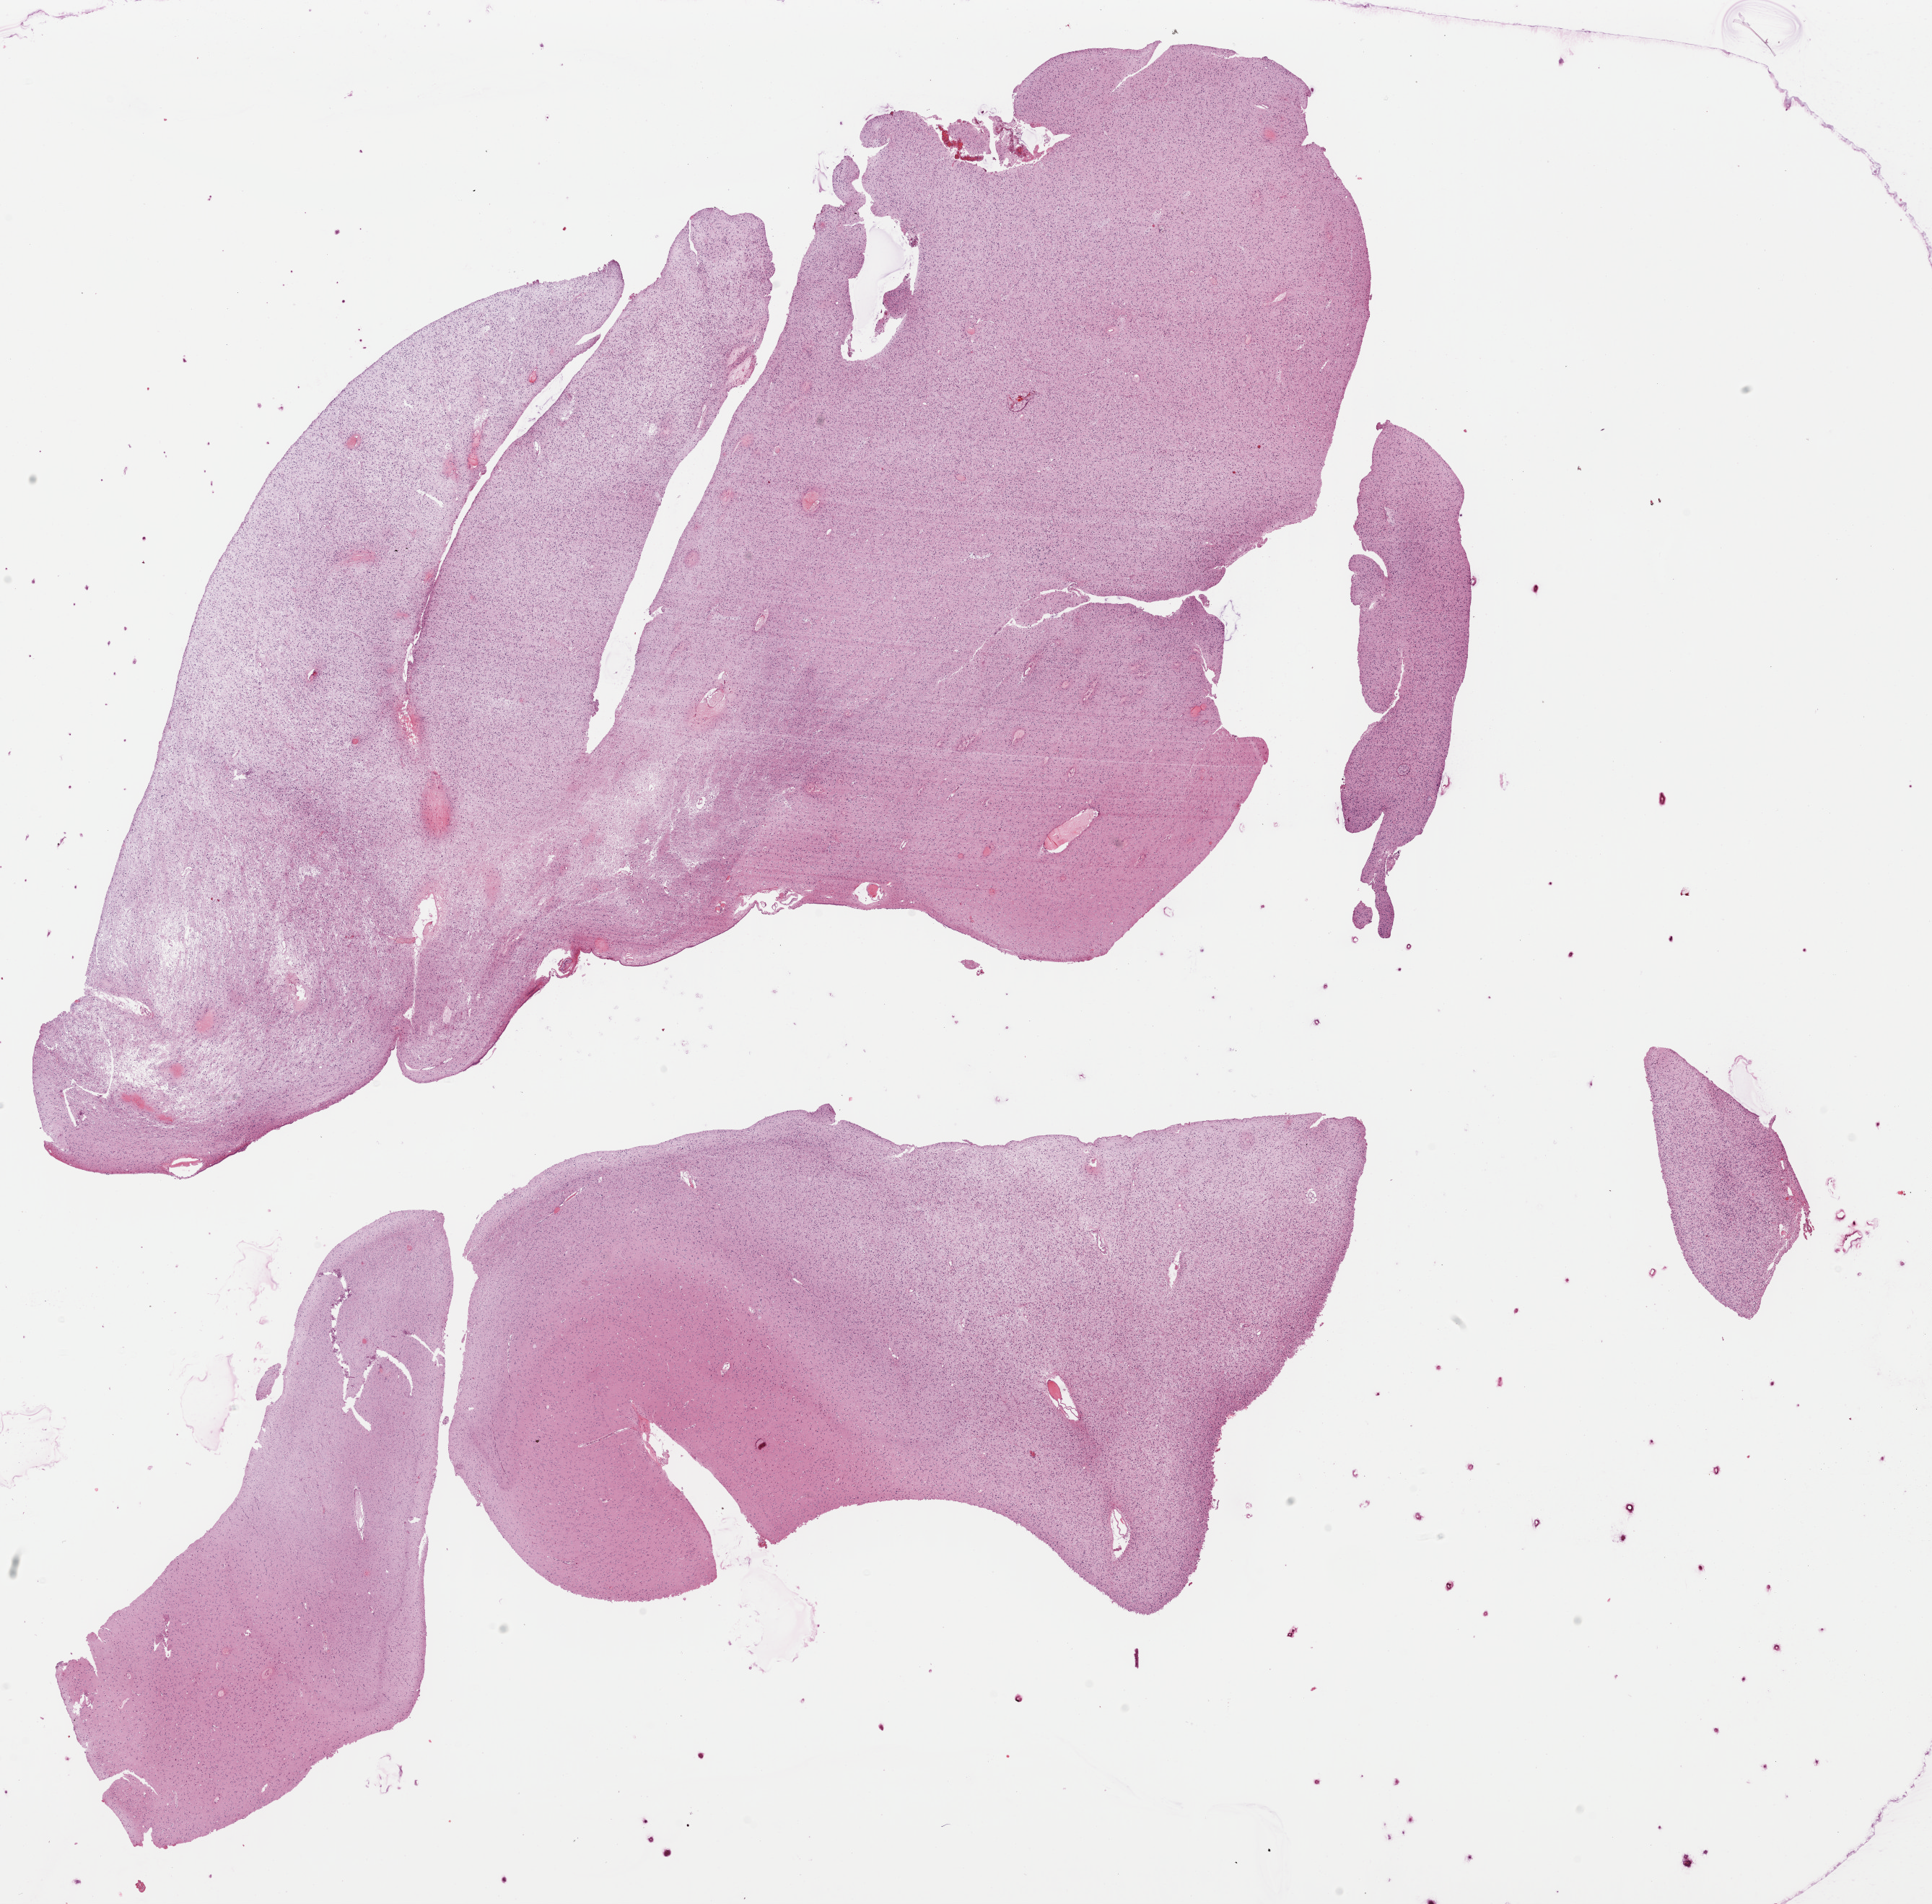
H&E whole-slide image, shown as a low-resolution overview of the whole scanned area (about 21.1 x 20.8 mm), FFPE section, sample: primary tumour, brain. Patient: male, age at initial diagnosis 43 years. Histologic grade: G3 (poorly differentiated).
* histologic diagnosis: Mixed glioma (cerebrum)
* laterality: right